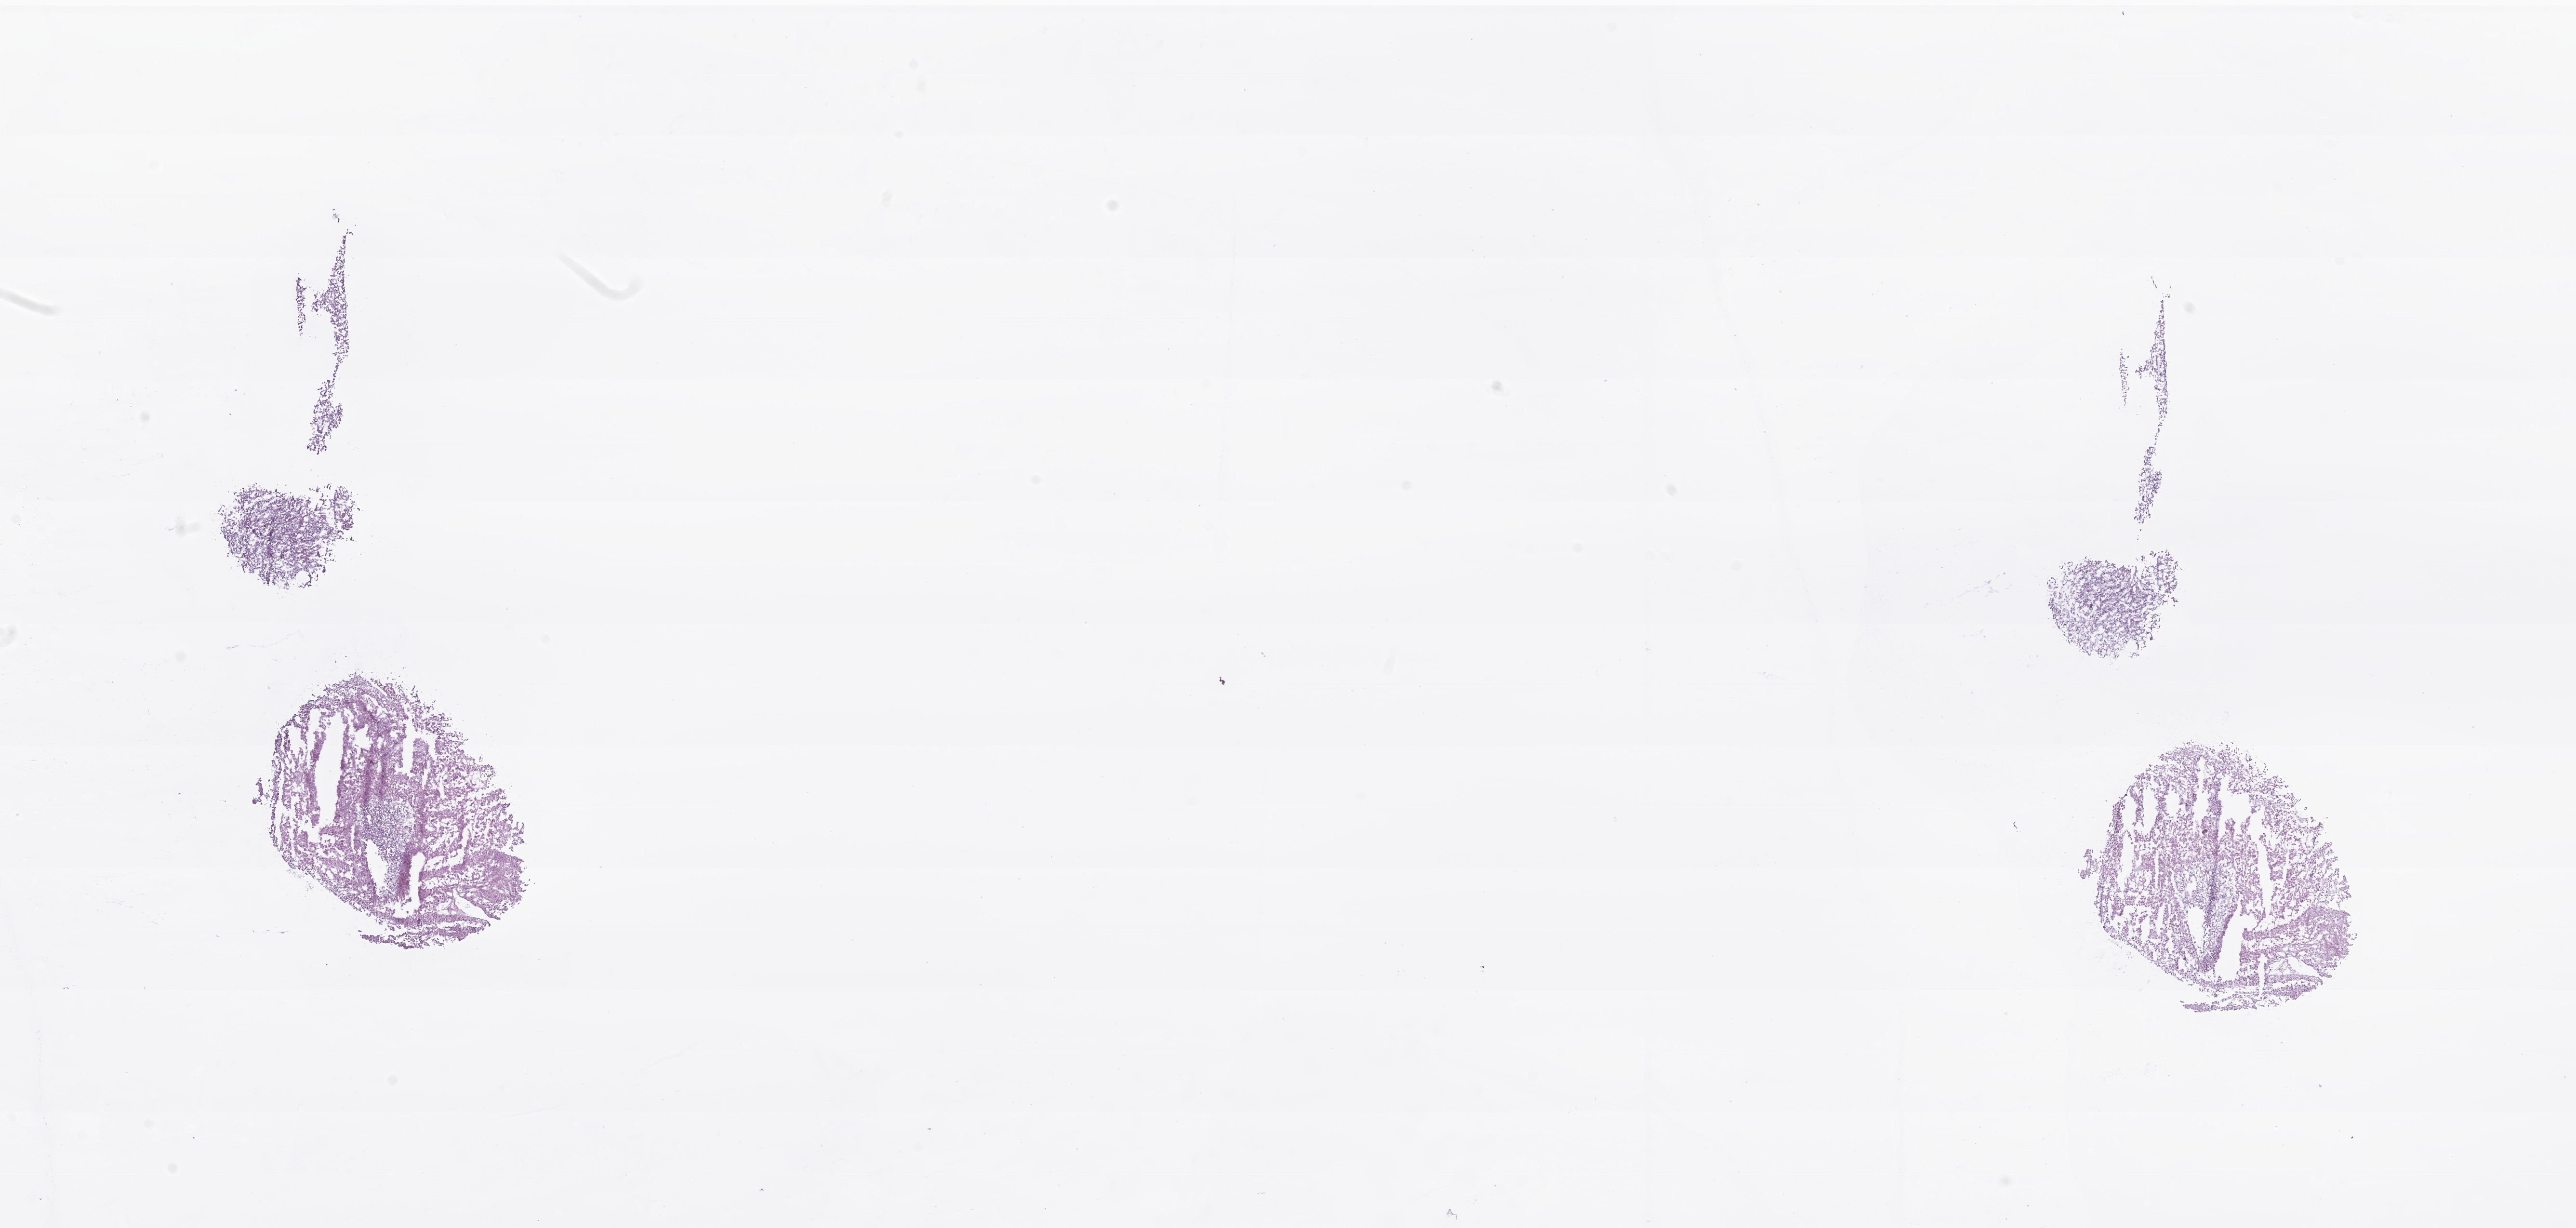
Digitized haematoxylin and eosin-stained section of tumor tissue from the adrenal gland — a low-resolution overview of the entire scanned area, about 22.5 x 10.7 mm, frozen section (OCT-embedded). Patient: male, age 78 months (6 years 6 months).
Recorded diagnosis: Adrenal cortical carcinoma.